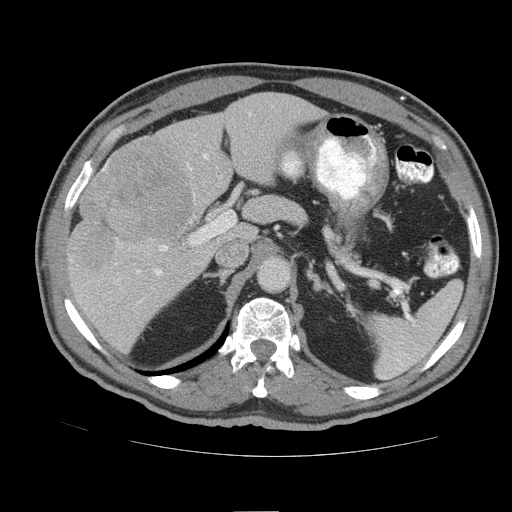
Contrast-enhanced abdominal CT (liver protocol), one axial slice; position 56 of 105 along the scan axis; soft-tissue window (W 400 / L 40 HU); 2.5 mm slice thickness; 512 × 512 image matrix, field of view 380 × 380 mm. From the clinical record (not read from this slice): diagnosis: hepatocellular carcinoma (patient treated with transarterial chemoembolisation; whether this scan precedes or follows treatment is not stated here); TNM stage (as recorded): Stage-IIIB; Child-Pugh class: A; tumour nodularity: multinodular.
Structures marked on this image (semi-automatically segmented with operator editing):
- liver parenchyma outside the tumour (the mass and vessels are separate outlines, so this box may not span the whole liver): box from (x=66, y=92) to (x=324, y=352) px
- mass: (x=71, y=139)–(x=196, y=270)
- liver vessels: (x=102, y=113)–(x=251, y=303)